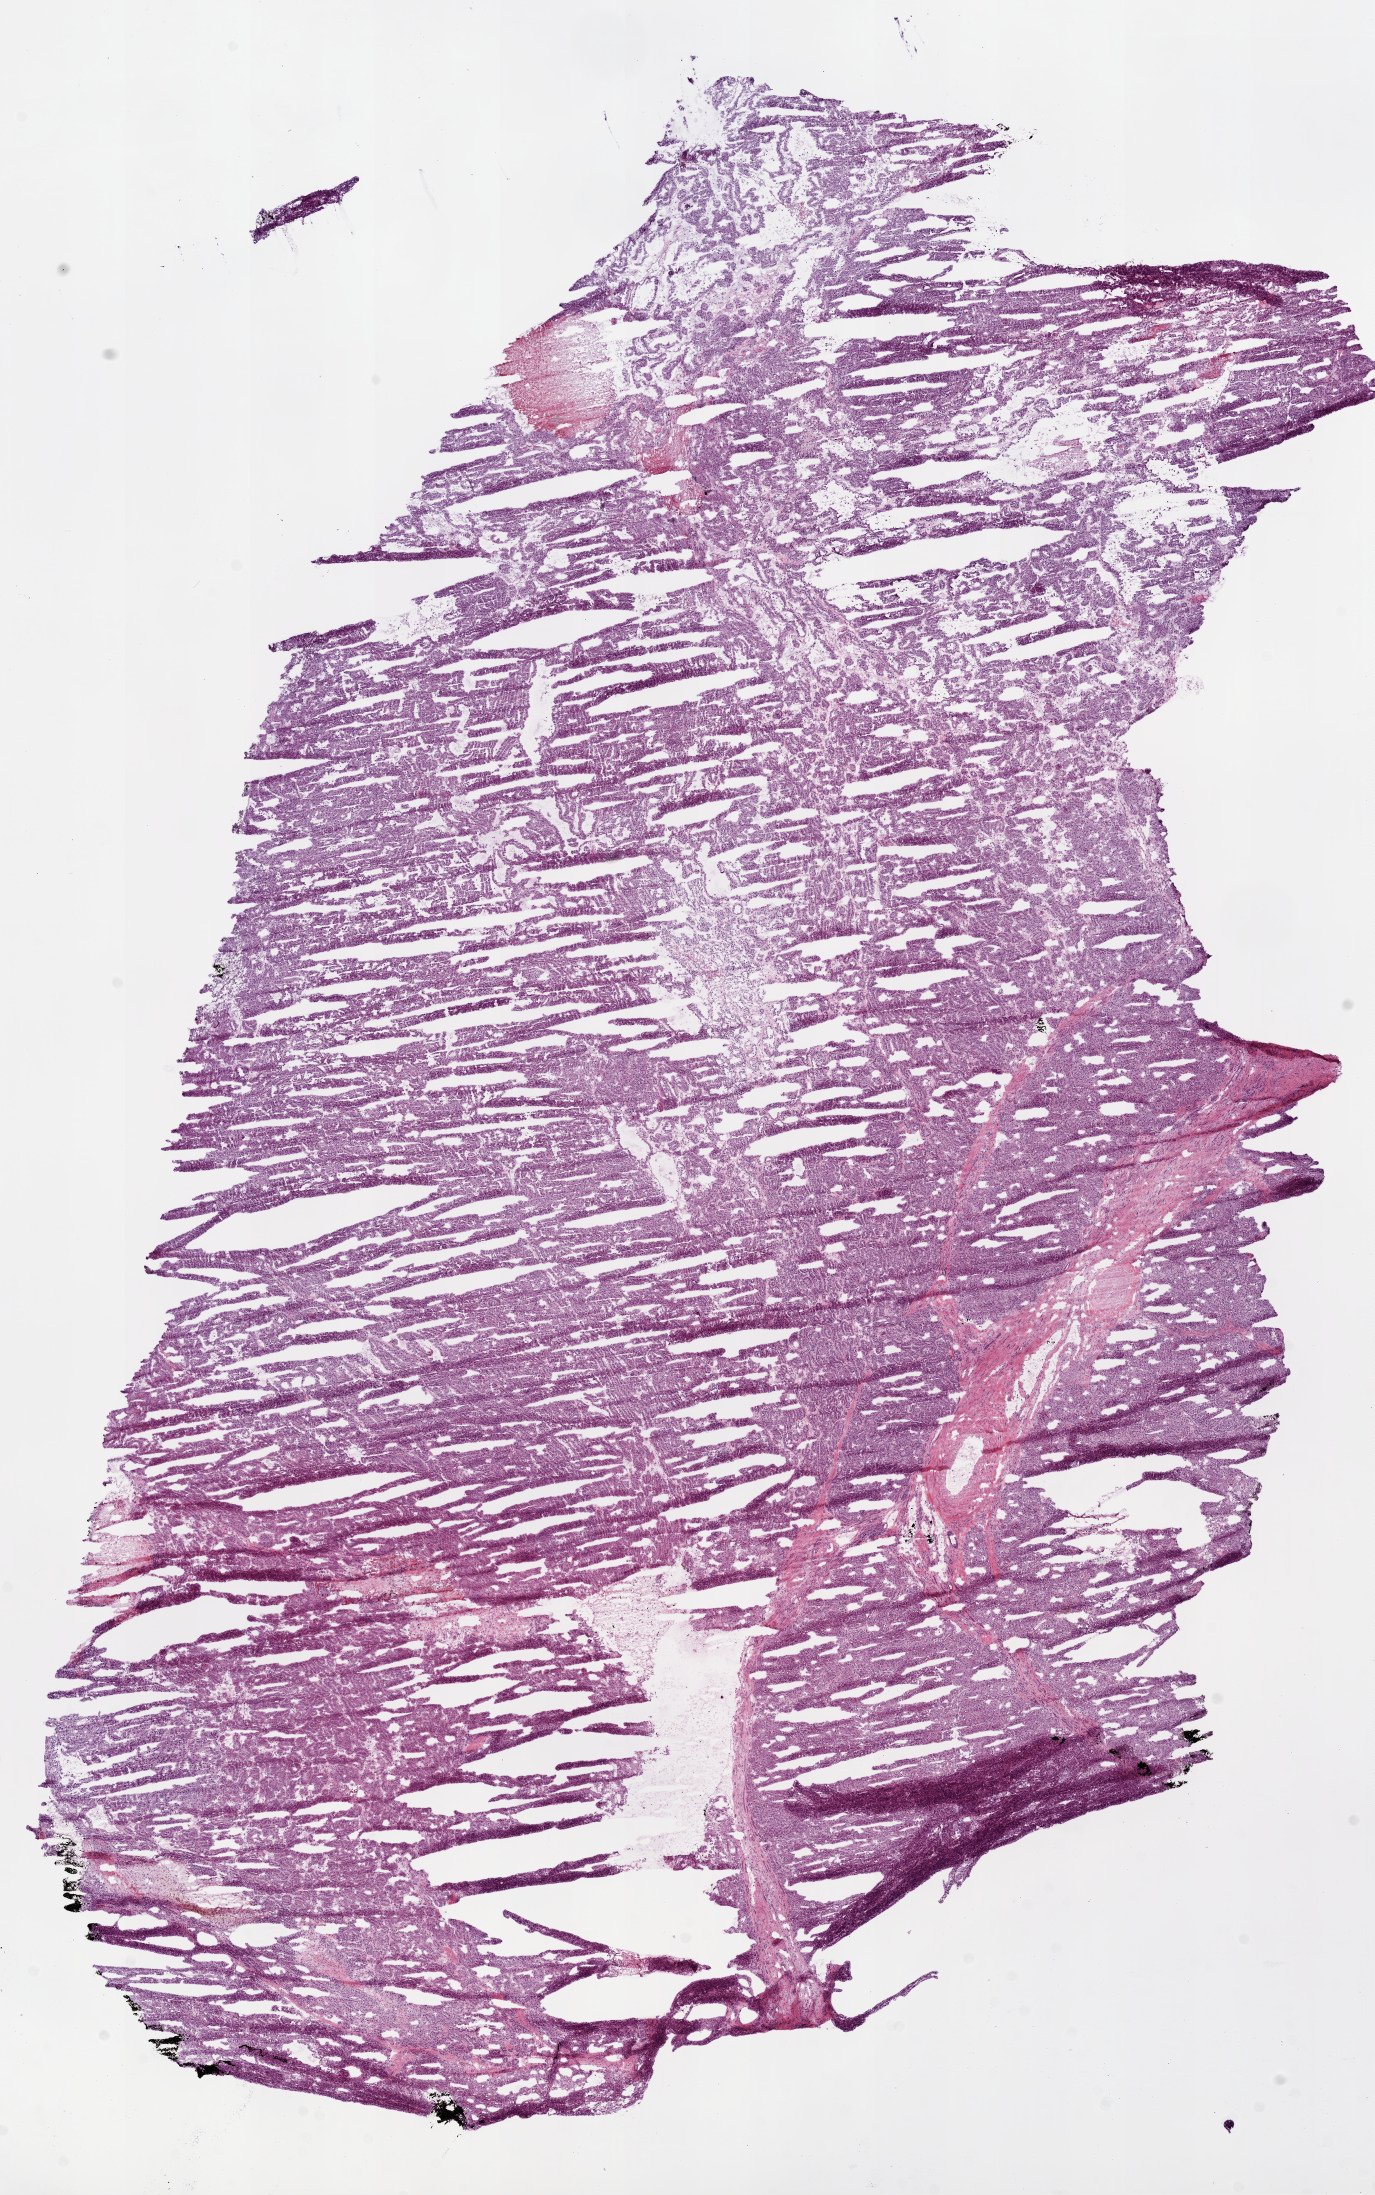
H&E whole-slide image — shown as a low-resolution overview of the whole scanned area (about 11.0 x 17.6 mm, acquisition: 20x scan), frozen section from the bottom of the tissue portion, primary tumour sample from the kidney. Male, age 59 years at initial diagnosis. Histologic grade: G3 (poorly differentiated). Slide review estimates, as recorded: tumour cells 90%, tumour nuclei 80%, normal cells 0%, stromal cells 10%, necrosis 0%.
- TNM: T1b N0 M0
- AJCC pathologic stage: I
- histologic diagnosis: Clear cell adenocarcinoma, NOS